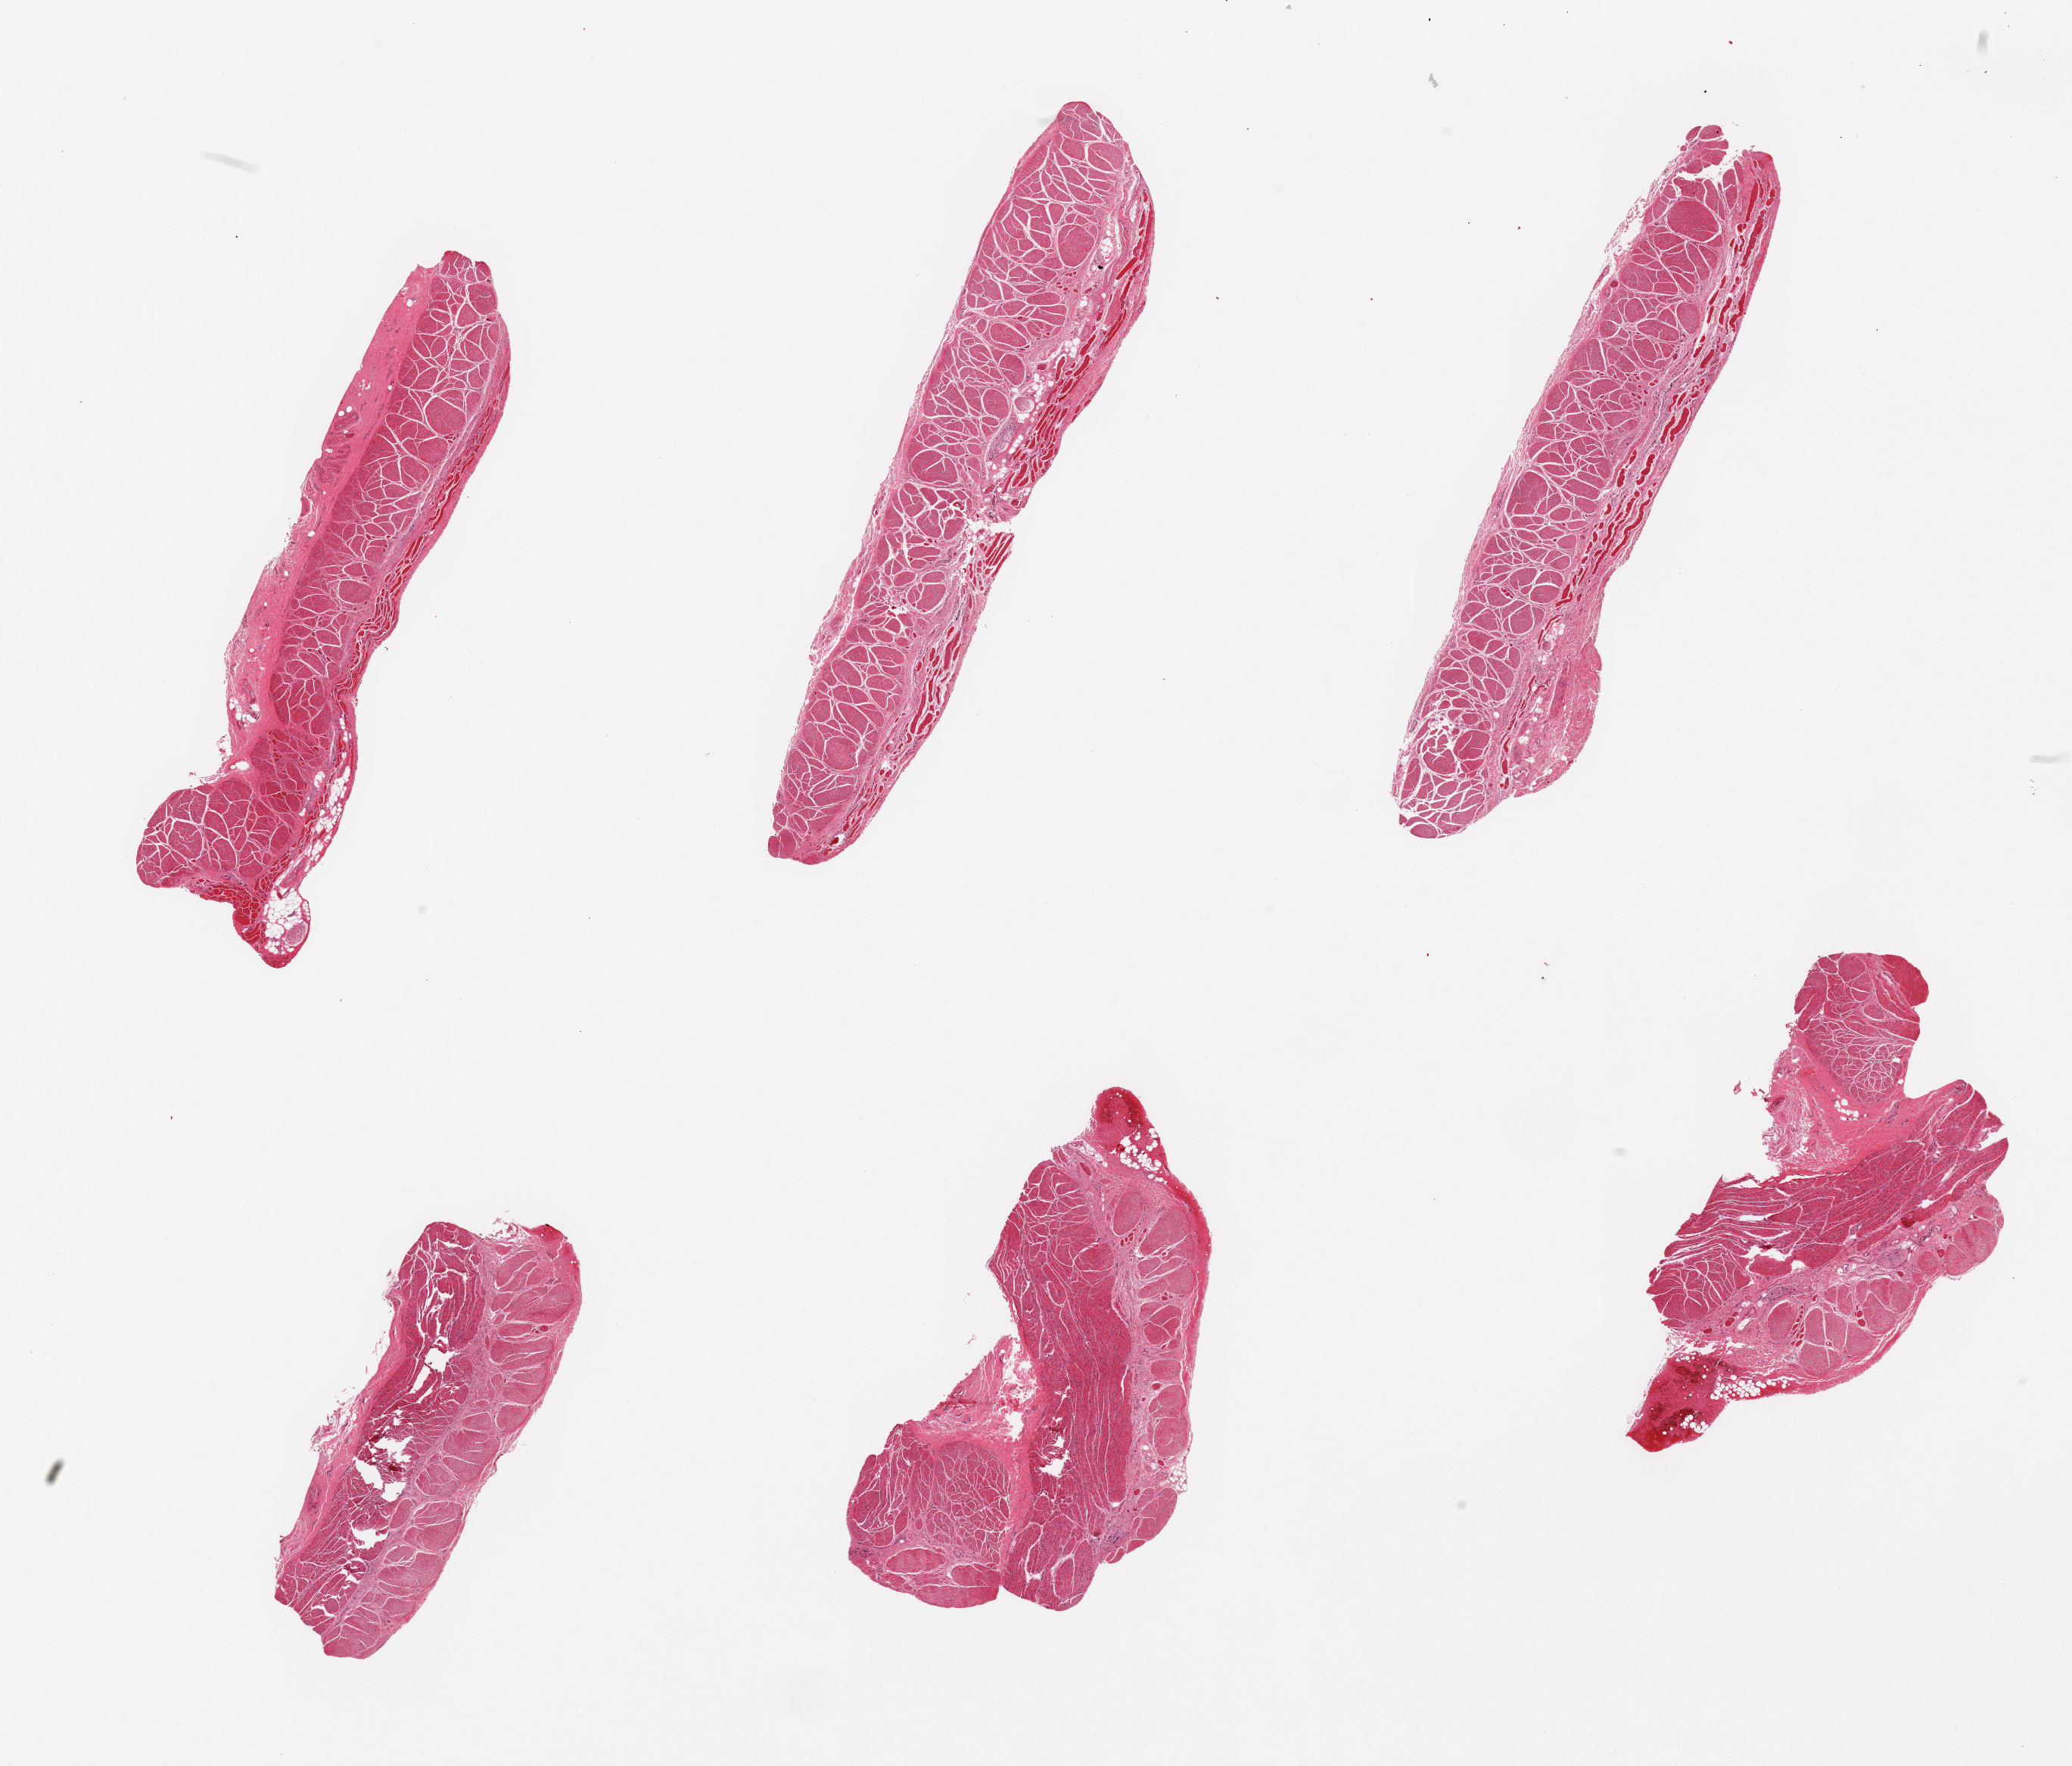
H&E whole-slide image, brightfield — shown as a low-resolution overview of the whole scanned area (about 21.7 x 18.5 mm, slide scanned at 20x). Male donor.
Specimen: PAXgene-fixed, paraffin-embedded tissue; section of esophageal muscle (target tissue); tissue donor sample.